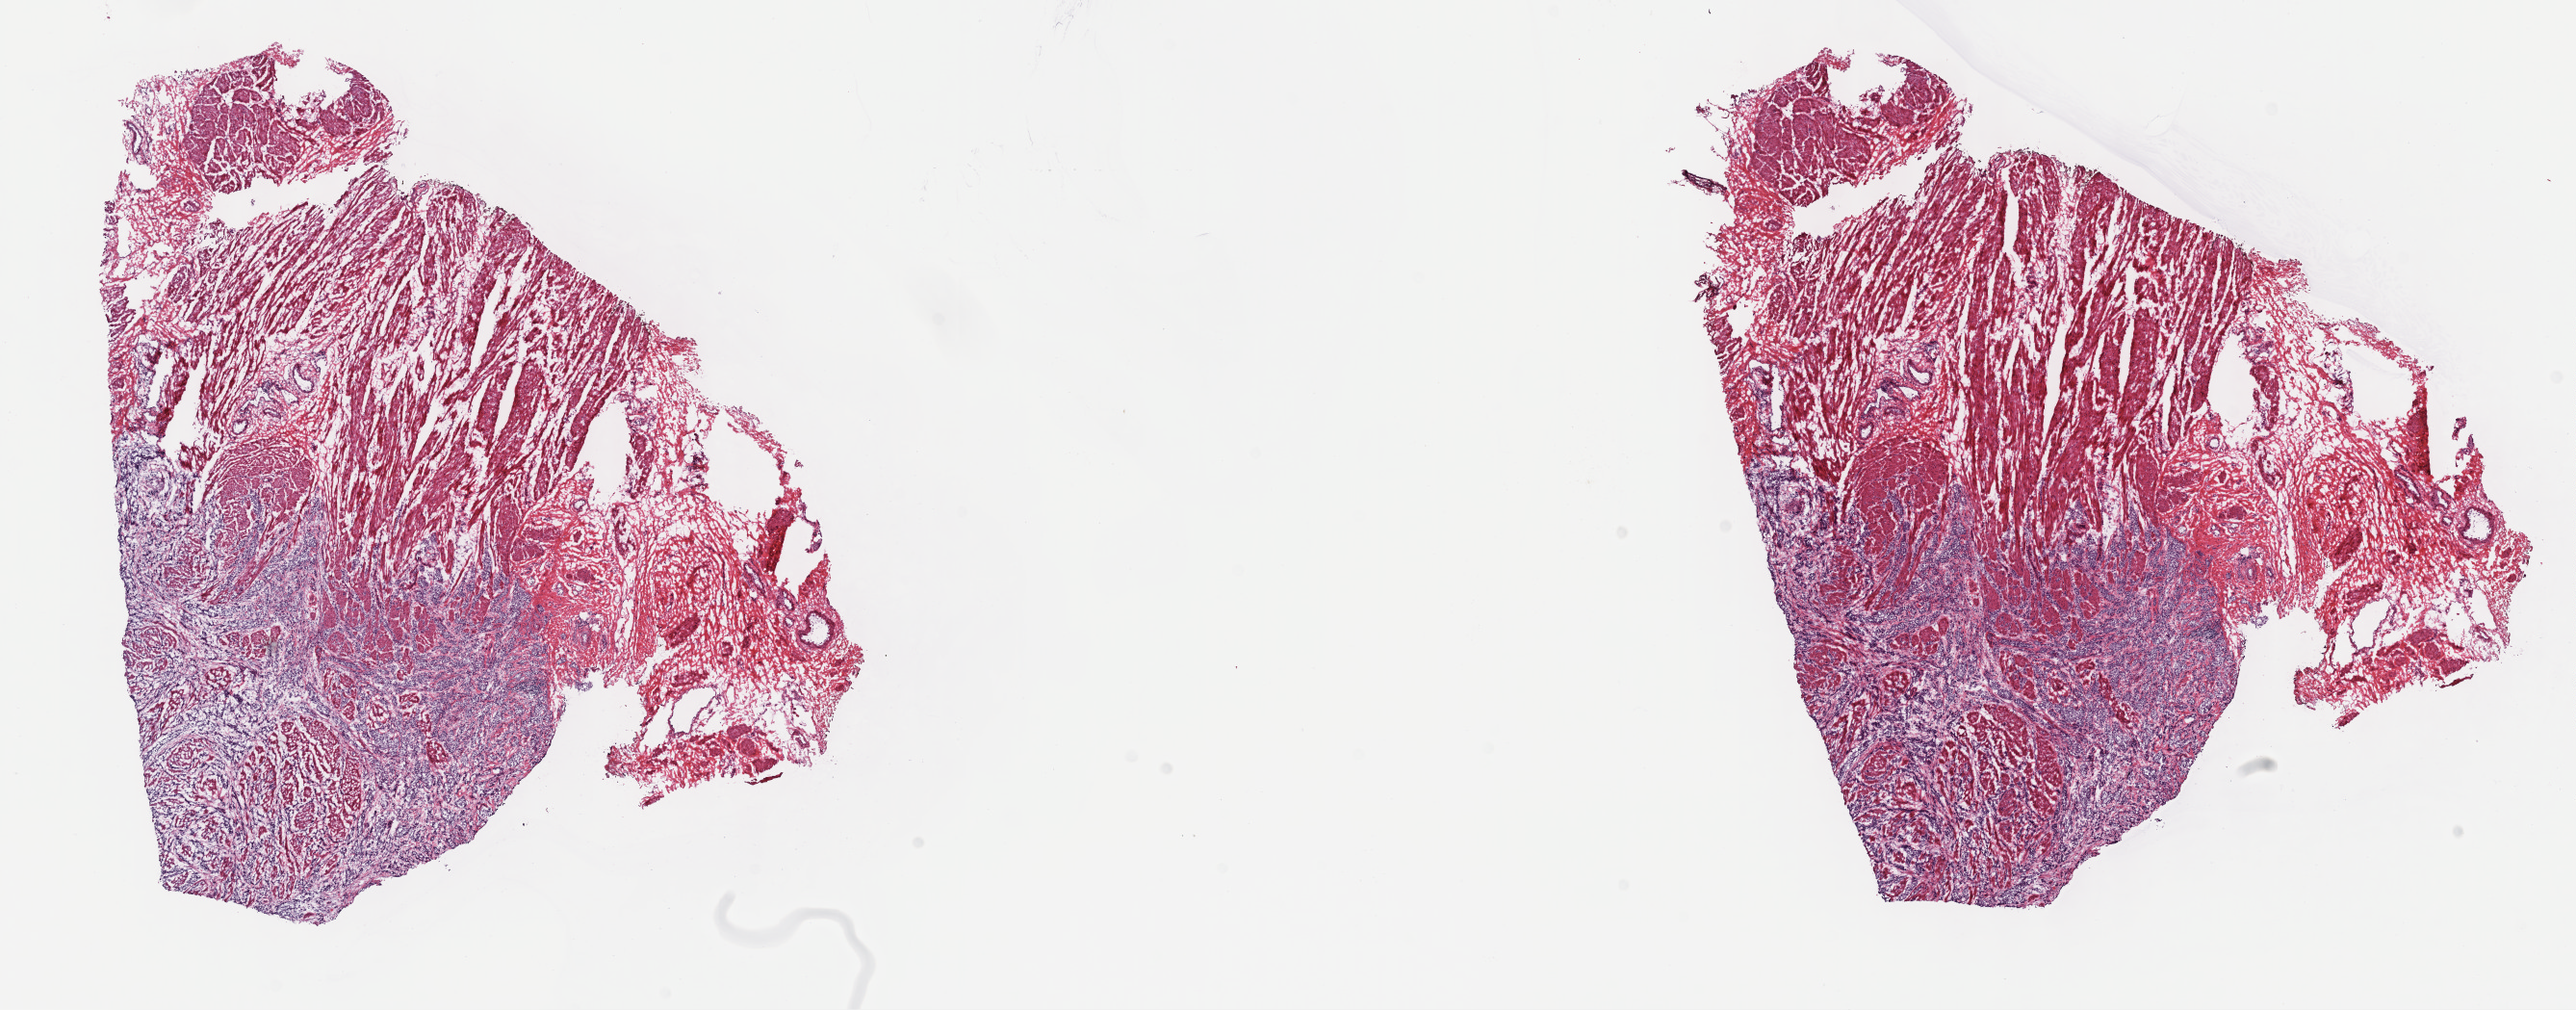
Hematoxylin and eosin (H&E) stained whole-slide image — low-resolution overview of the scanned area, about 21.6 x 8.5 mm. Frozen section from the top of the tissue portion. Primary tumour sample from the bladder. Male patient; age at initial diagnosis 48 years. Histologic grade: high grade. Composition of this section per pathologist review: tumour cells 28%, tumour nuclei 95%, normal cells 0%, stromal cells 70%, necrosis 2%. Infiltration values recorded for this section: lymphocyte infiltration 3%, monocyte infiltration 0%, neutrophil infiltration 0%.
* diagnosis: Transitional cell carcinoma
* AJCC pathologic stage: III (6th edition)
* TNM: T3b N0 MX